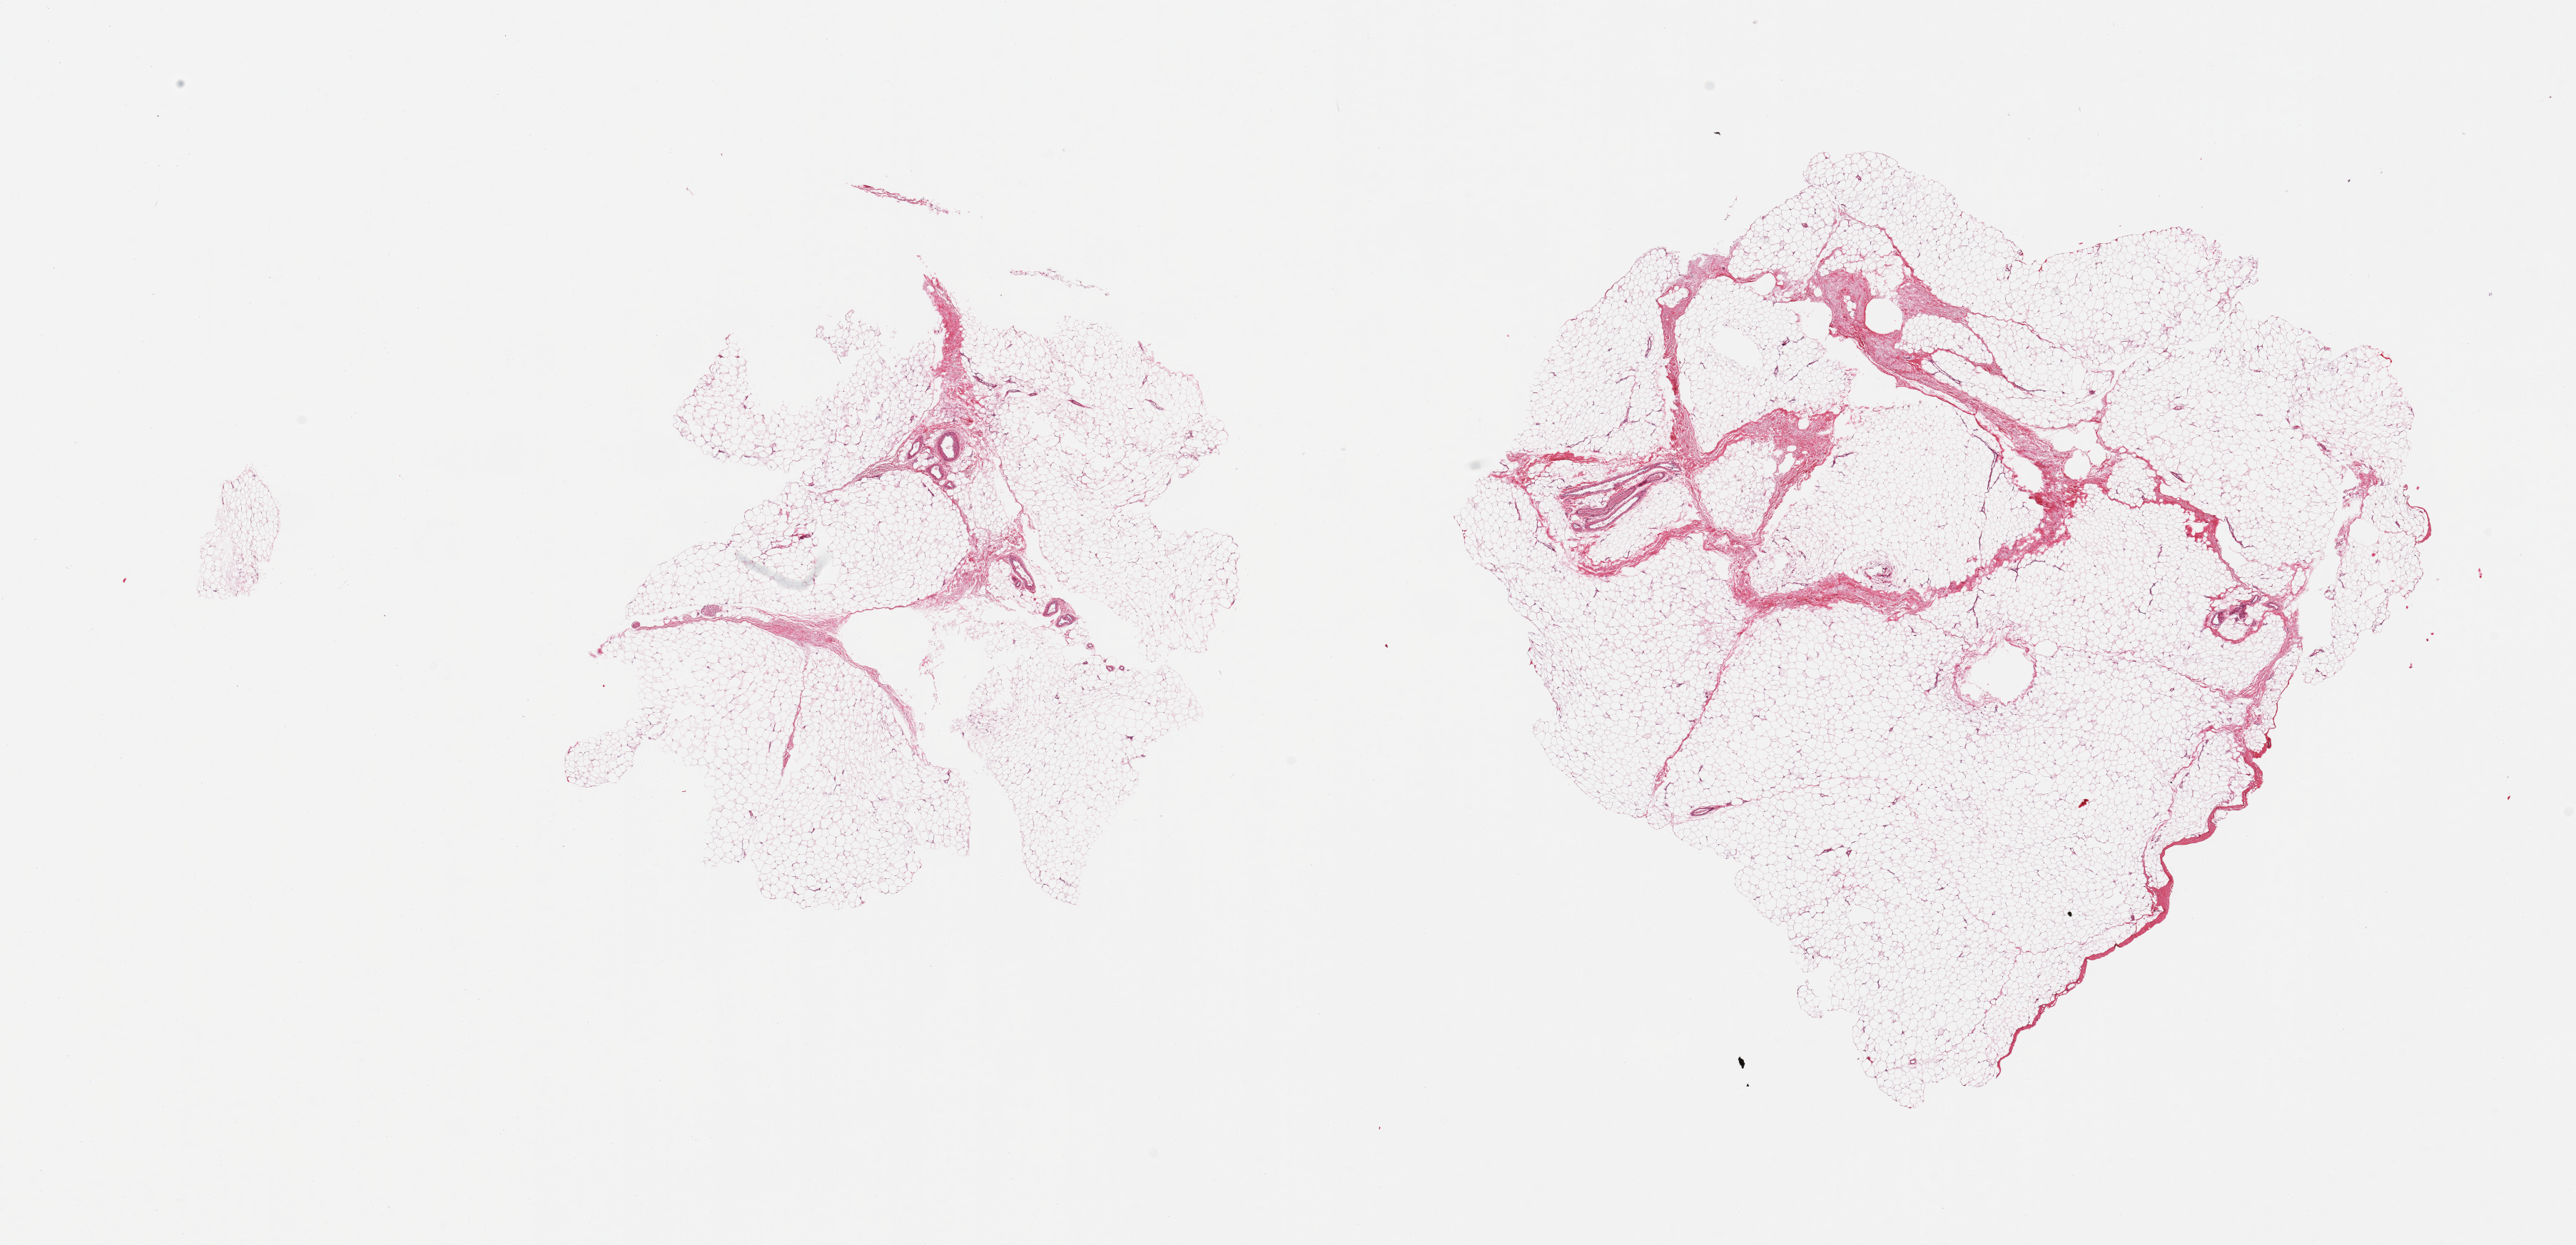
Haematoxylin and eosin whole-slide image, shown as a low-resolution overview of the whole scanned area (about 28.5 x 13.8 mm). Donor: male.
Specimen: PAXgene-fixed paraffin-embedded (PFPE) section; section of adipose tissue (target tissue); donor tissue sample.